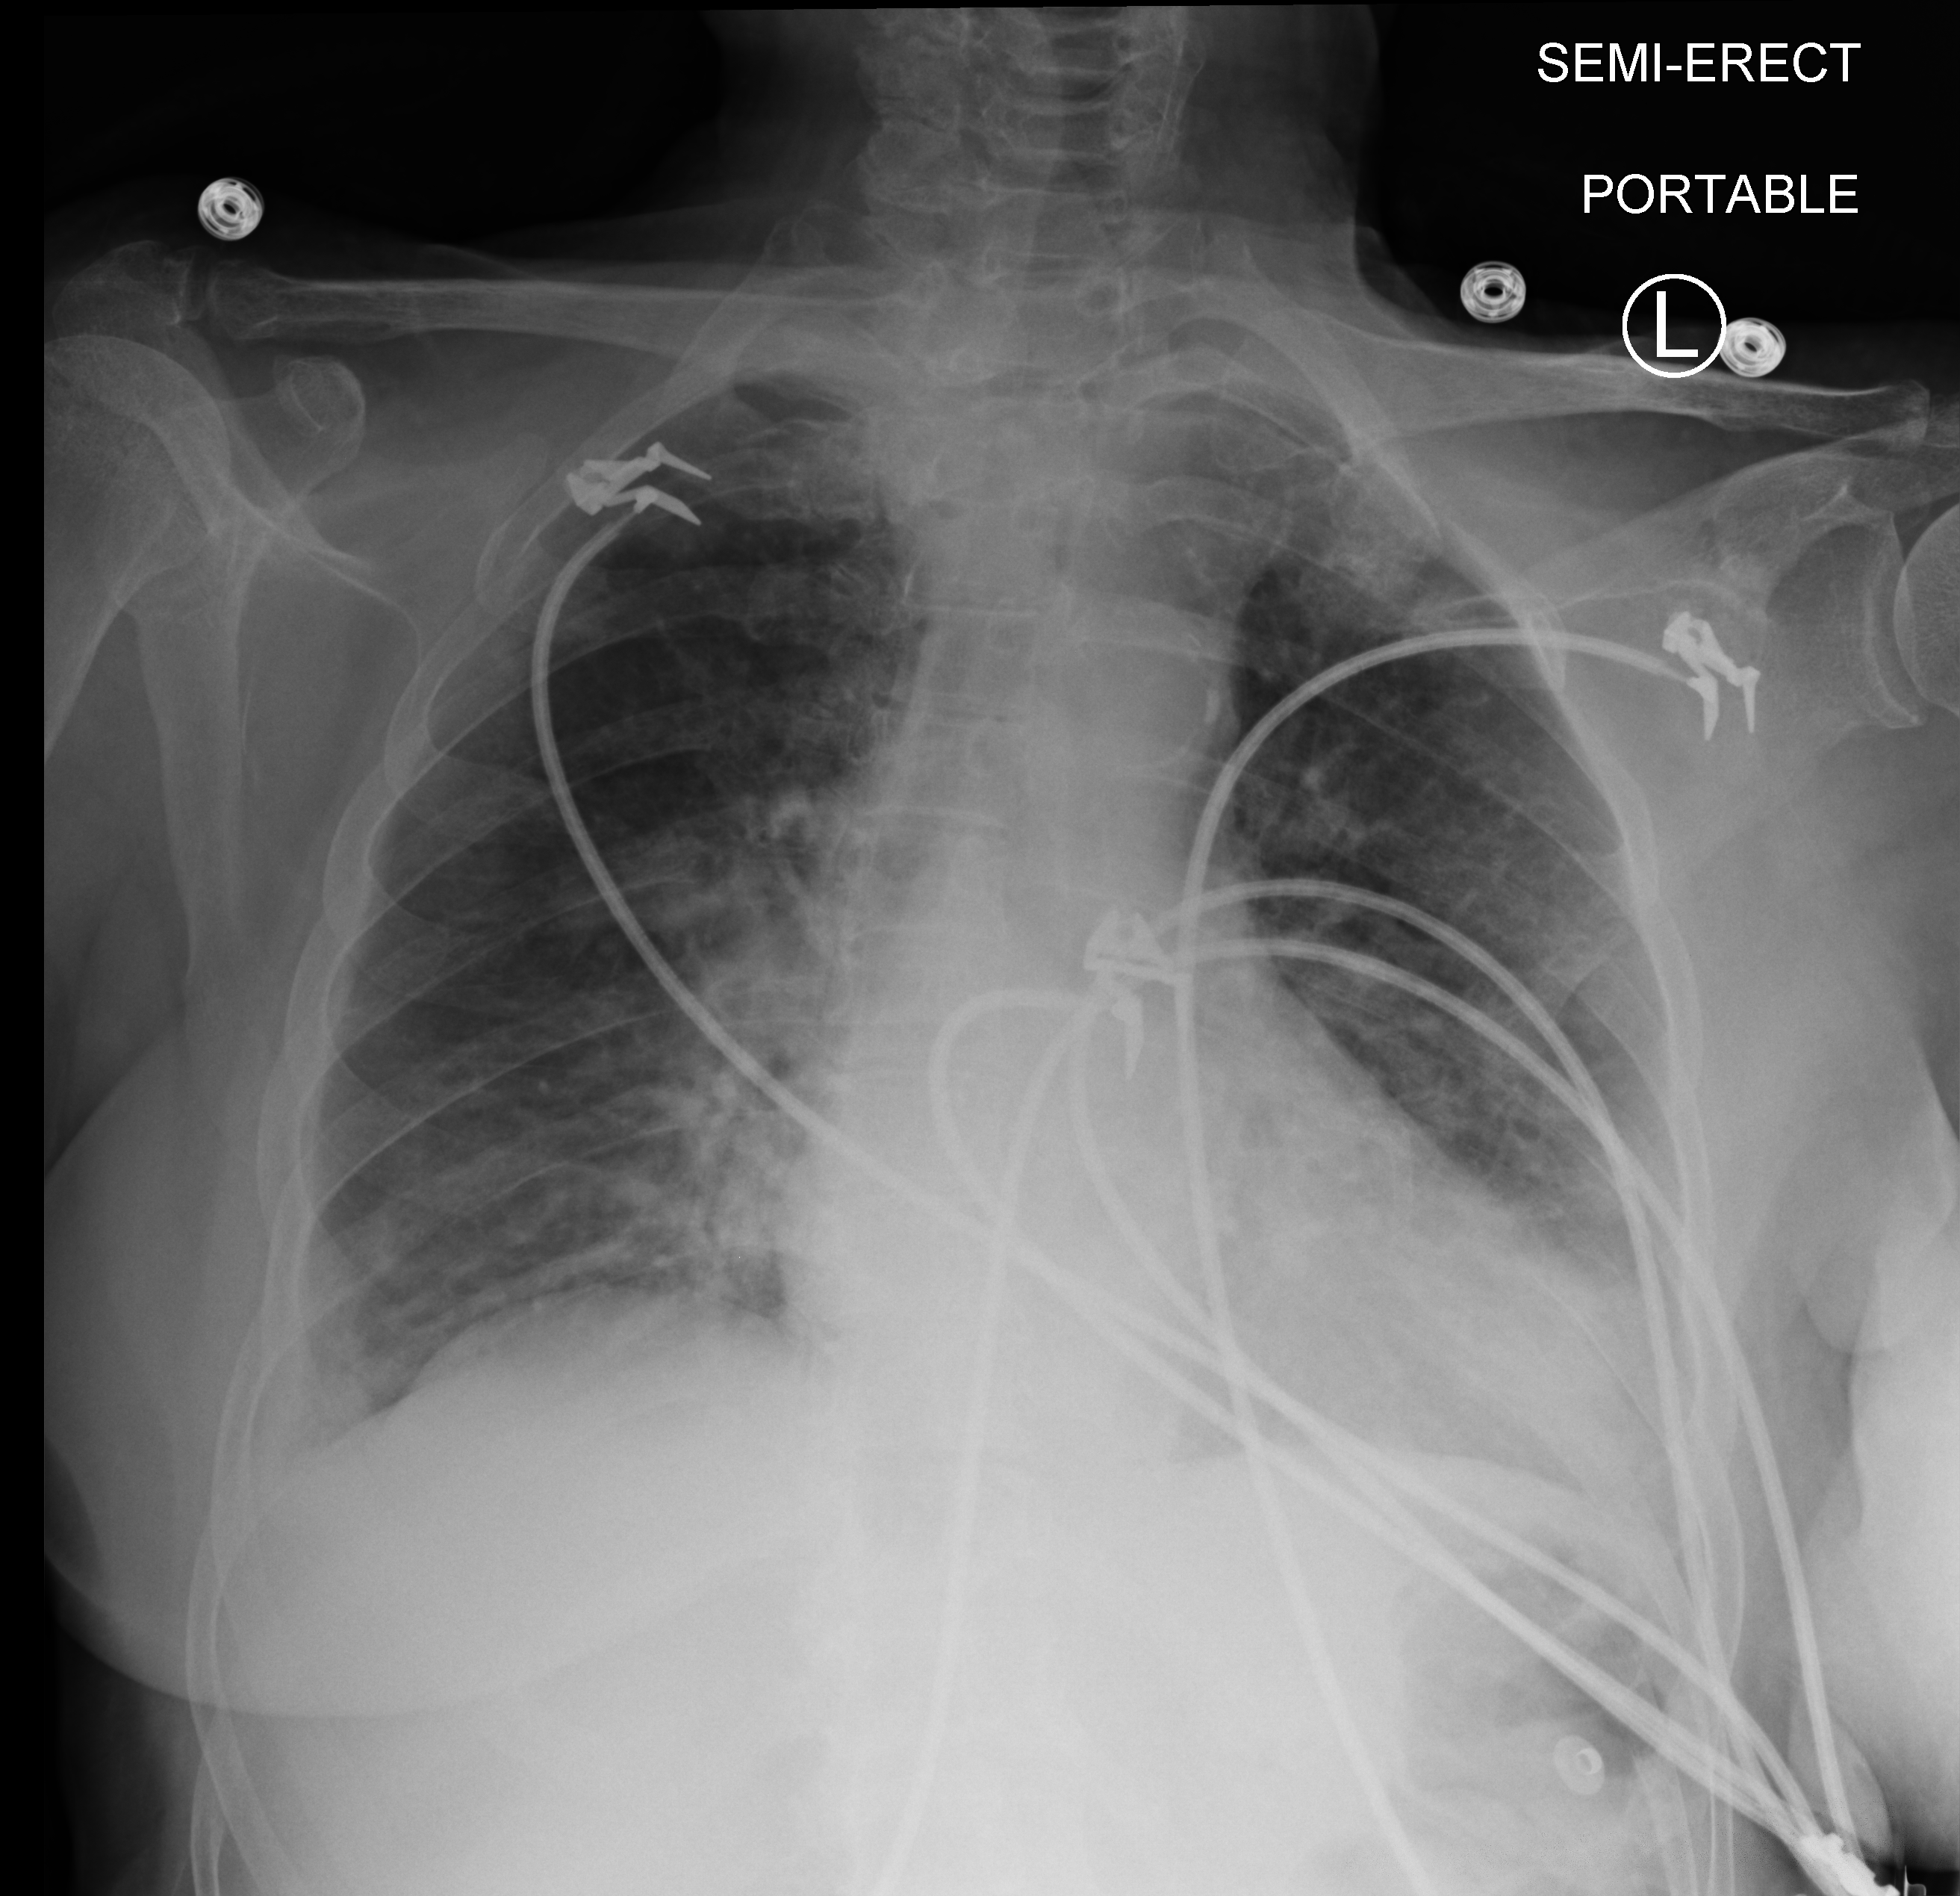
Chest X-ray (portable). Patient hospitalised with COVID-19; female, aged 60–74 years.
Hospital-stay facts (about this admission, not read from this image; timing relative to this image not recorded):
- length of hospital stay: 10 days
- admitted to intensive care during this hospital stay: no